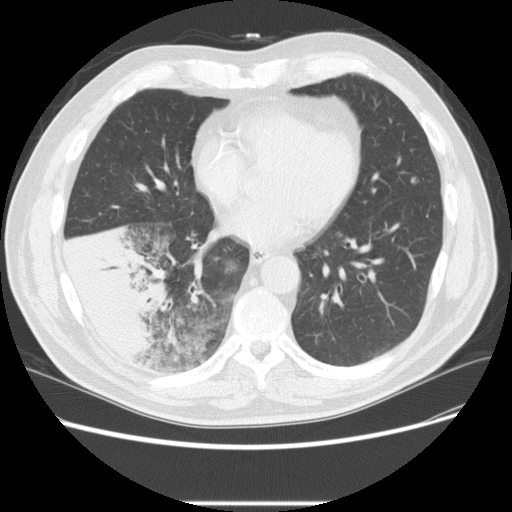
Low-dose screening chest CT, one axial slice; position 92 of 233 along the scan axis; reconstruction kernel STANDARD; 120 kVp; lung window (W 1500 / L -600 HU); 512 × 512 image matrix, field of view 380 × 380 mm.
Structures marked on this image (expert manual segmentation):
- lesion 3 (tumor, lower lobe of right lung): box from (x=65, y=226) to (x=167, y=355) px